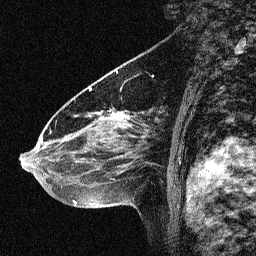
Breast MRI (dynamic contrast-enhanced), one sagittal slice; position 39 of 64 along the scan axis; dynamic contrast-enhanced study with each time point stored as its own series, time point 2 of 3 at this slice position (early post-contrast, ordered by acquisition time); 1.5 T; TE 4.5 ms, TR 11 ms; 2.06 mm slice thickness; 256 × 256 image matrix, field of view 200 × 200 mm. Female patient, age 46 years. Case-level facts recorded for this patient, not image findings: setting: breast cancer imaged before/during neoadjuvant chemotherapy; receptor status: HER2-positive.
Structures marked on this image (semi-automatically segmented with operator editing):
- analysis volume of interest (the breast-tissue region the enhancement analysis was run in; not a lesion): bounding box <42,80,150,180> (left, top, right, bottom; pixels)
- tumour enhancement mask (voxels above the 90 % enhancement threshold inside the analysis volume of interest): <88,117,131,180>